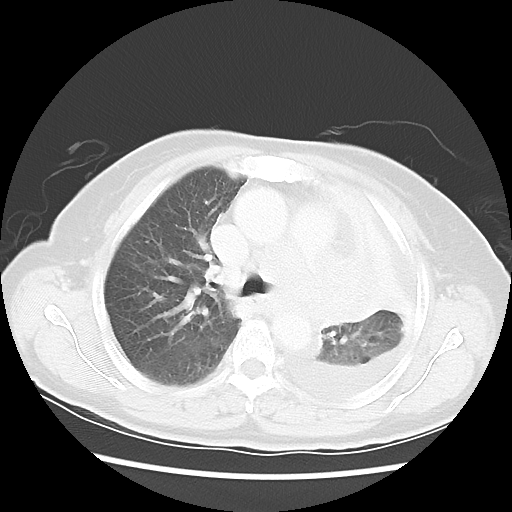
Chest CT, one axial slice; reconstruction kernel LUNG; lung window (W 1500 / L -600 HU); 5 mm slice thickness; 512 × 512 image matrix, field of view 336 × 336 mm. Female patient, age 72 years. Case-level facts recorded for this patient, not image findings: clinical TNM (as recorded): T4 N3 M1b.
Outlined on this slice (bounding box drawn by a radiologist):
- lung tumour (recorded histology: large cell carcinoma): bounding box [x1, y1, x2, y2] px = [281, 248, 403, 336]